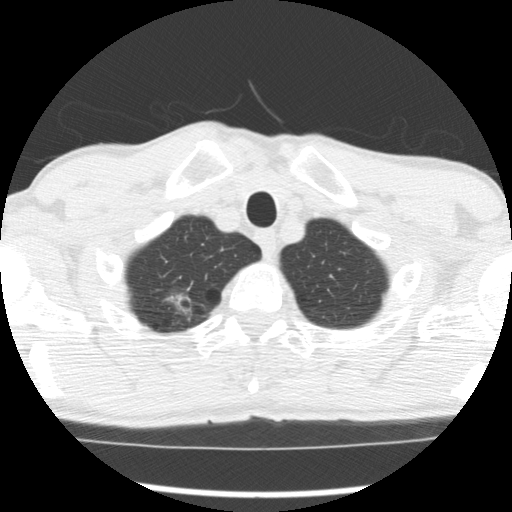
Low-dose screening chest CT, axial slice, baseline screening round, lung window (W 1500 / L -600 HU), slice 23 of 277 in the series. Male participant, aged 66 years at enrolment.
Lesion marked by an expert reader, bounding box <150,284,204,333> (left, top, right, bottom; pixels). The screening reader recorded 4 non-calcified nodules or masses ≥4 mm on this exam; which of them this box marks is not recorded. Official screen result: positive, change unspecified: nodule(s) >= 4 mm or enlarging nodule(s), mass(es), or other non-specific abnormalities suspicious for lung cancer. Participant outcome: lung cancer diagnosed 503 days after this screen — adenocarcinoma, NOS, right upper lobe, undifferentiated (G4), stage IA (AJCC 6th edition), 20 mm at pathology.